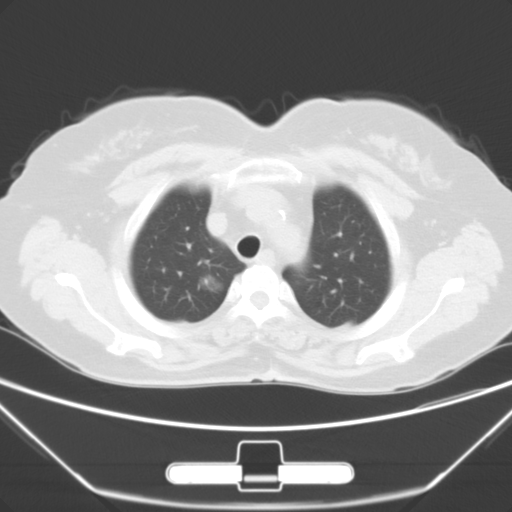
Chest CT, one axial slice; position 46 of 55 along the scan axis; 120 kVp; lung window (W 1500 / L -600 HU); 5 mm slice thickness; 512 × 512 image matrix, field of view 356 × 356 mm. Patient: female, 63 years. From the clinical record (not read from this slice): clinical TNM (as recorded): T1a N0 M0.
Outlined on this slice (bounding box drawn by a radiologist):
- lung tumour (recorded histology: adenocarcinoma): box from (x=196, y=270) to (x=228, y=298) px